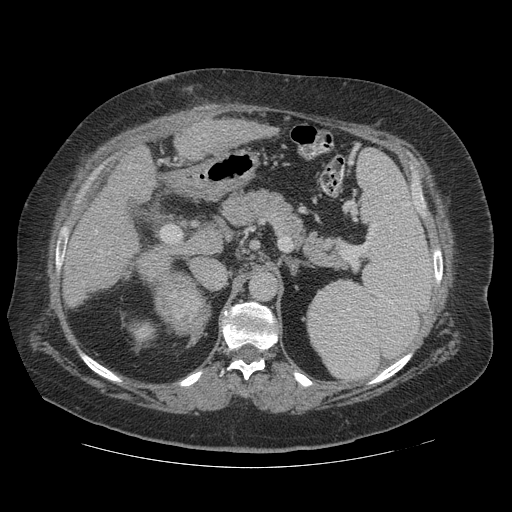
Contrast-enhanced abdominal CT (liver protocol), one axial slice; slice 67 of 121 in the series (ordered by position); reconstruction kernel STANDARD; soft-tissue window (W 400 / L 40 HU); 2.5 mm slice thickness; 512 × 512 image matrix, field of view 420 × 420 mm. Case-level facts recorded for this patient, not image findings: diagnosis: hepatocellular carcinoma (patient treated with transarterial chemoembolisation; whether this scan precedes or follows treatment is not stated here); TNM stage (as recorded): Stage-IIIA; Child-Pugh class: A; tumour differentiation: well differentiated; tumour size: 7.4 cm.
Outlined on this slice (semi-automatically segmented with operator editing):
- liver parenchyma outside the tumour (the mass and vessels are separate outlines, so this box may not span the whole liver): bounding box [x1, y1, x2, y2] px = [70, 118, 278, 273]
- mass: [158, 278, 211, 336]
- liver vessels: [95, 230, 110, 254]